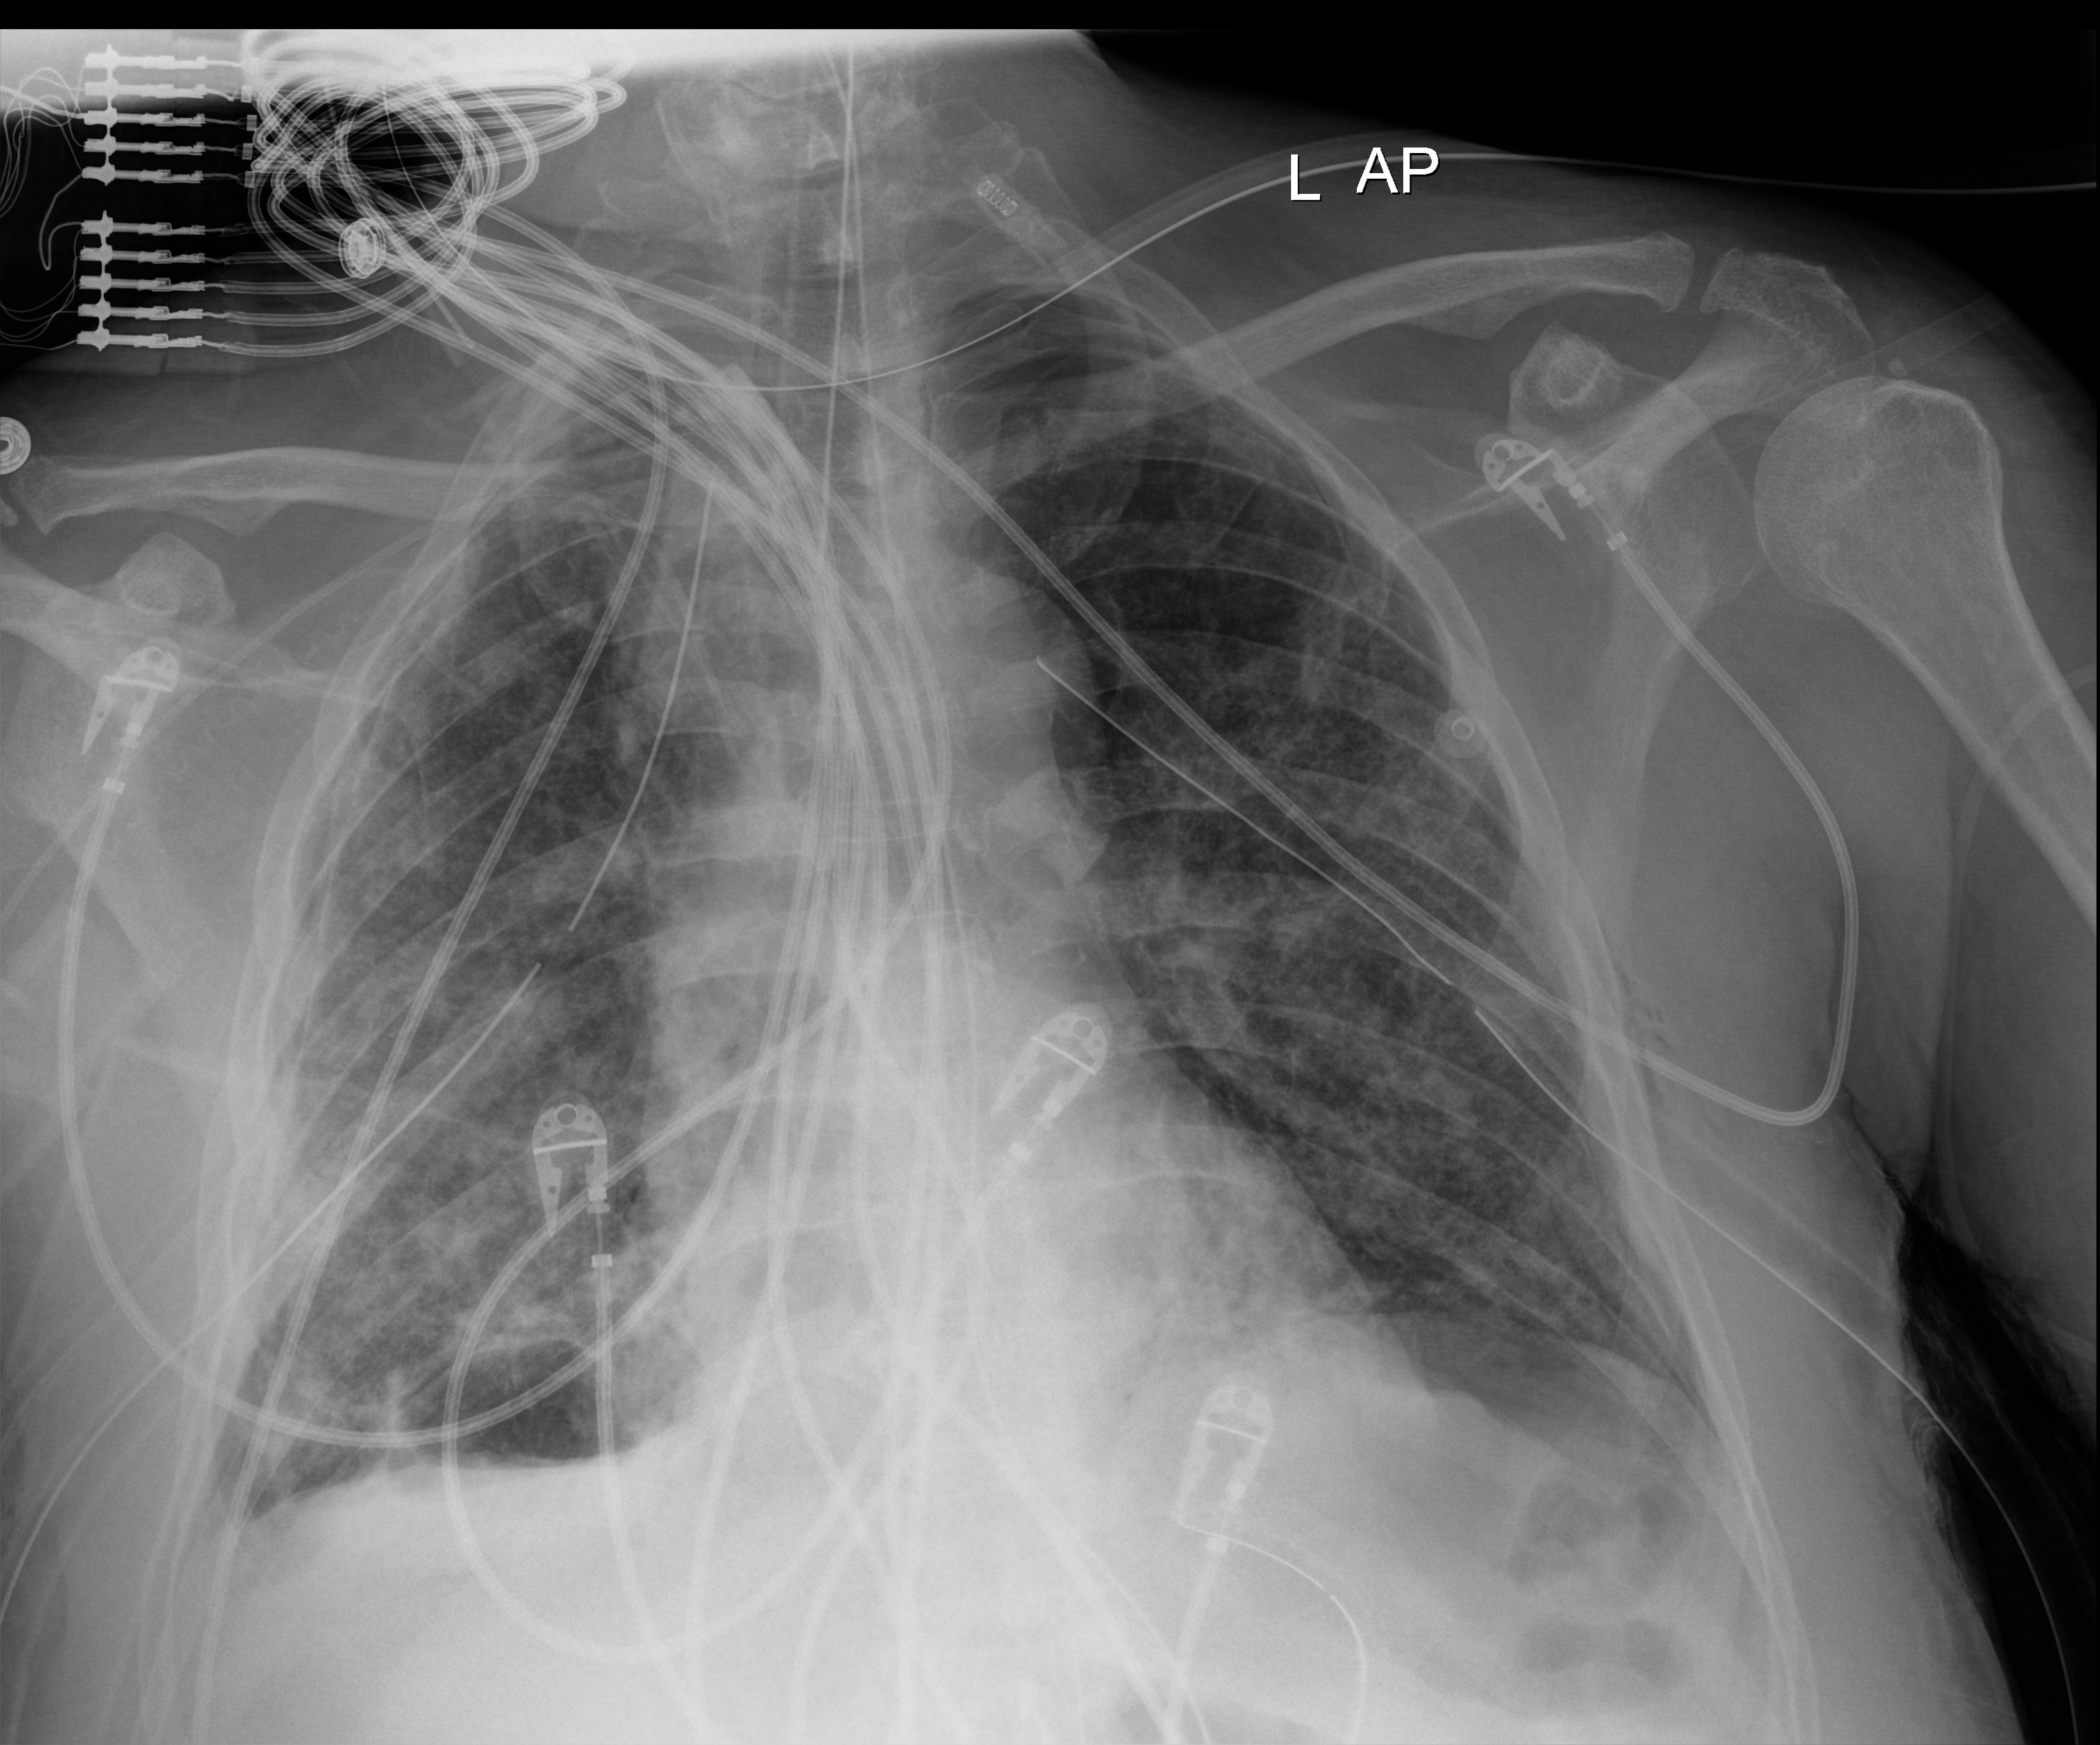
Chest X-ray (portable); anteroposterior (AP) projection. Male patient hospitalised with COVID-19, age 60–74 years.
Hospital-stay facts (about this admission, not read from this image; timing relative to this image not recorded):
- chronic kidney disease (admission record): no
- admitted to intensive care during this hospital stay: yes